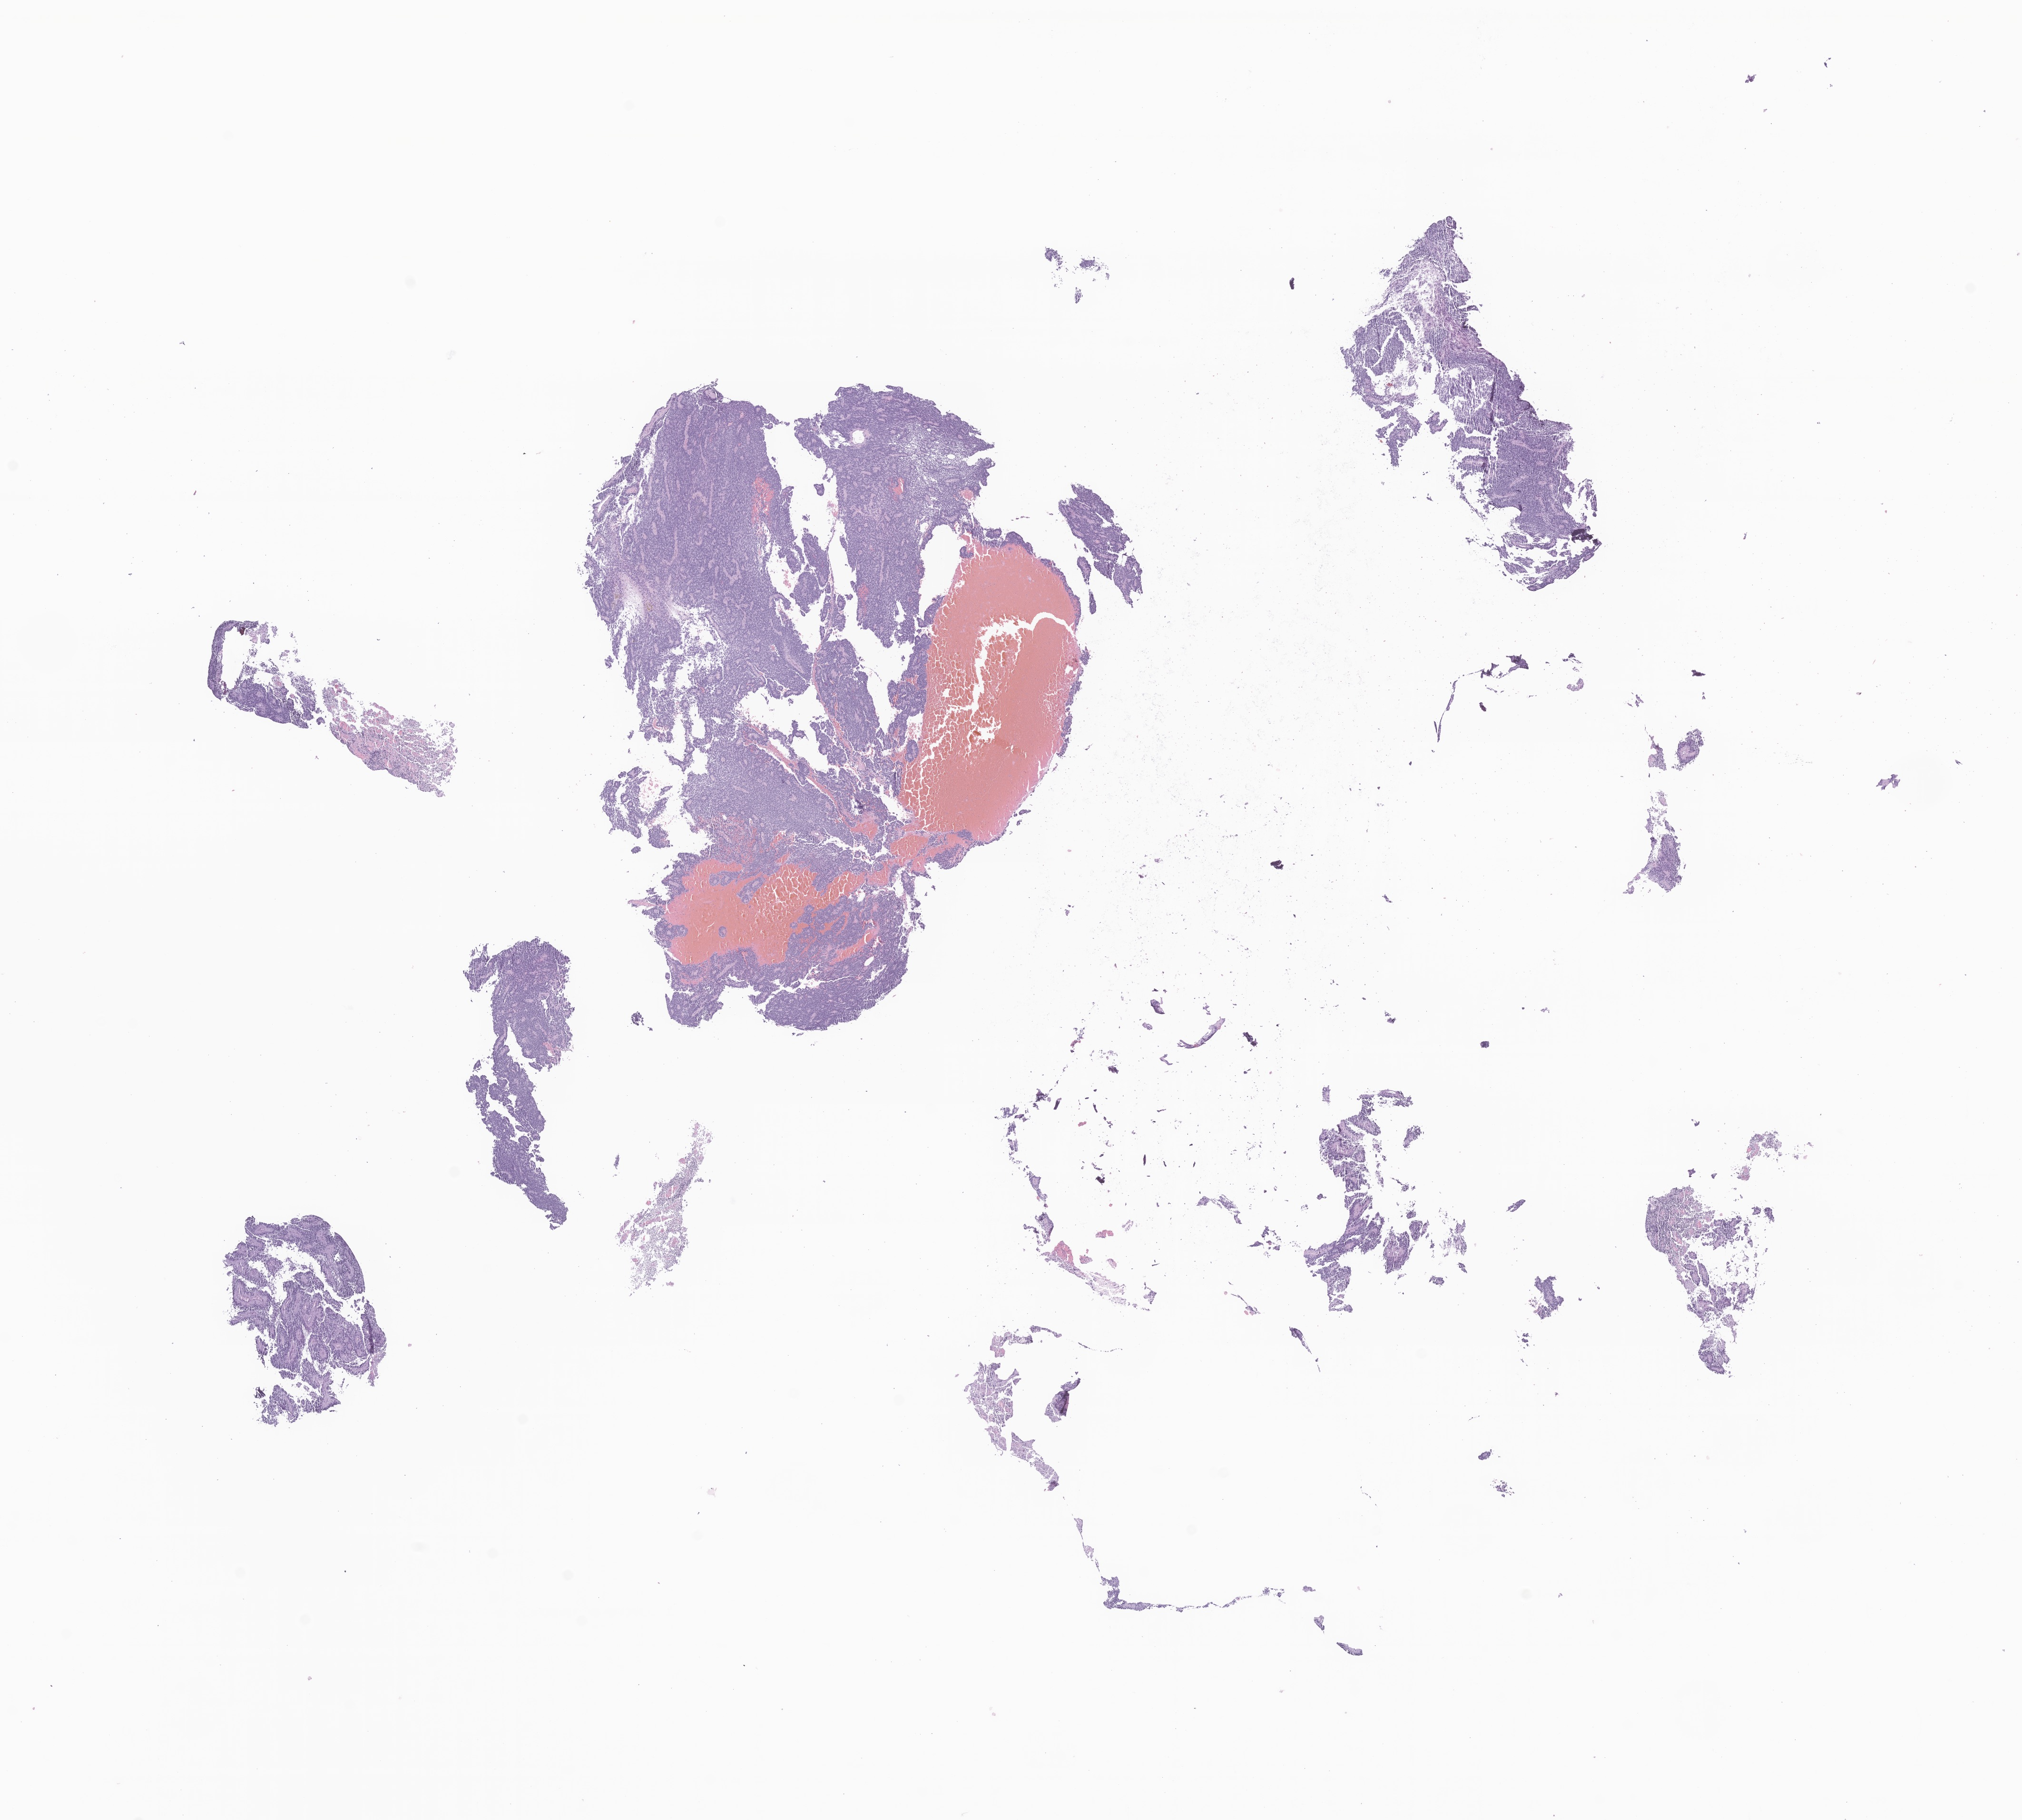
H&E whole-slide image of tumor tissue from the brain, a low-resolution overview of the entire scanned area, about 17.9 x 16.1 mm; formalin-fixed, paraffin-embedded (FFPE) tissue. Male patient, age 62 months (5 years 2 months).
Diagnosis: Ependymoma, NOS.